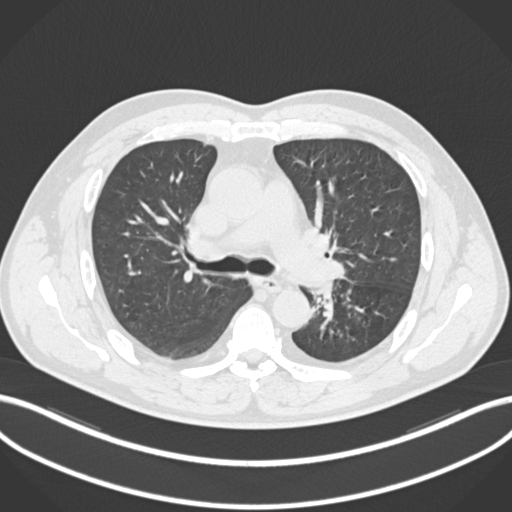
Chest CT, one axial slice. Position 144 of 223 along the scan axis. Reconstruction kernel B30f. 120 kVp. Lung window (W 1500 / L -600 HU). 1 mm slice thickness. 512 × 512 image matrix. Male patient, age 50 years. From the clinical record (not read from this slice): clinical TNM (as recorded): T2a N3 M0.
Annotated regions visible in this slice (bounding box drawn by a radiologist):
- lung tumour (recorded histology: squamous cell carcinoma): bounding box [x1, y1, x2, y2] px = [305, 275, 337, 327]